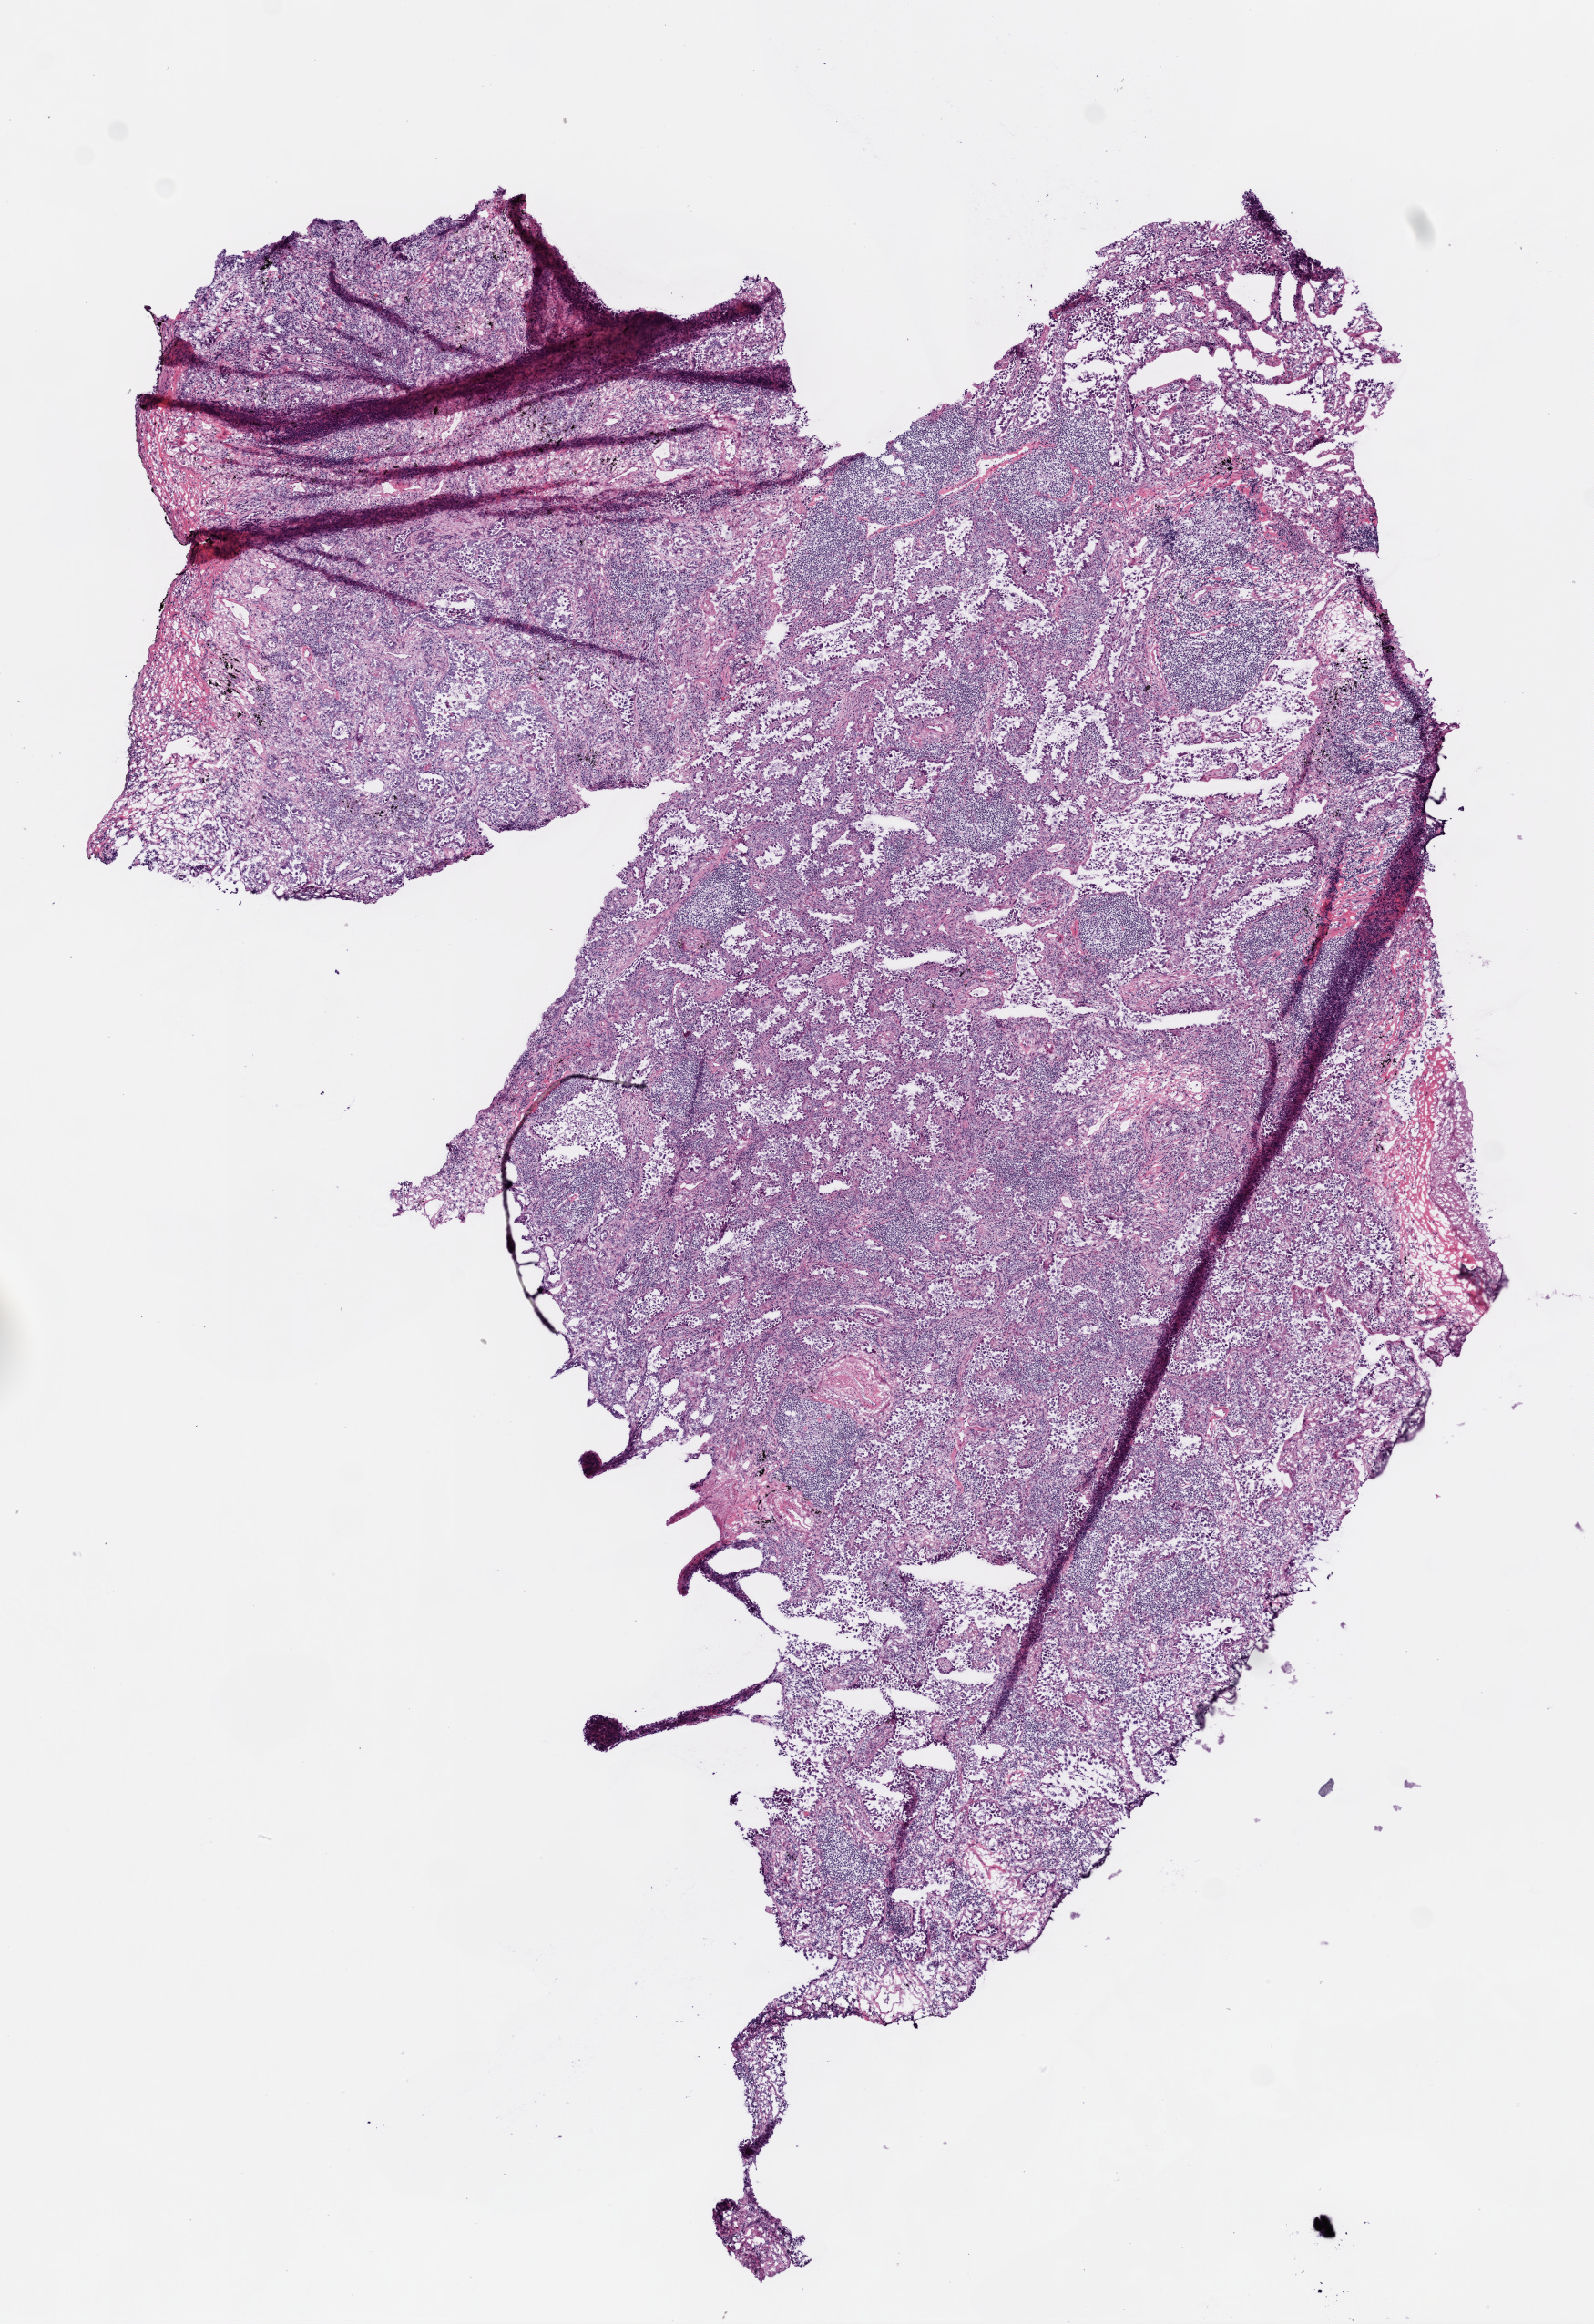
Digitized Hematoxylin and eosin (H&E) stained tissue section (whole slide), whole scanned area (about 7.0 x 10.2 mm) shown as a low-resolution overview; frozen section from the bottom of the tissue portion; lung, primary tumour sample. Female patient; age at initial diagnosis 74 years. Slide review estimates, as recorded: tumour cells 88%, tumour nuclei 75%, normal cells 0%, stromal cells 12%, necrosis 0%. Infiltration values recorded for this section: lymphocyte infiltration 20%.
Diagnosis: Adenocarcinoma, NOS (upper lobe, lung). AJCC pathologic stage: IB (6th edition). TNM: T2 NX M0.